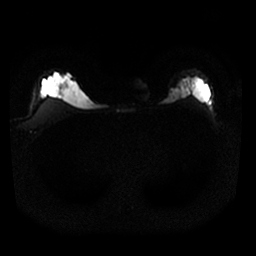
Breast MRI, one axial slice. Position 23 of 25 along the scan axis. Diffusion-weighted series; image 2 of 4 stored at this slice position (different b-values; order by instance number). 1.5 T. 256 × 256 image matrix, field of view 320 × 320 mm. Female patient.
Outlined on this slice (manually delineated by an expert):
- tumour on diffusion-weighted imaging: box from (x=173, y=92) to (x=186, y=100) px